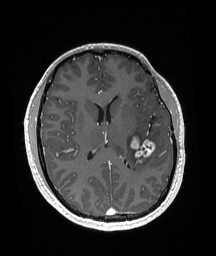
Brain MRI from a brain-tumour surgery series, one axial slice; slice 80 of 192 in the series (ordered by position); T1-weighted post-contrast; 216 × 256 image matrix, field of view 211 × 250 mm. From the clinical record (not read from this slice): histopathology: Glioneuronal tumor; WHO grade: 2.
Outlined on this slice (manually delineated by an expert):
- tumour: bounding box <130,137,156,164> (left, top, right, bottom; pixels)